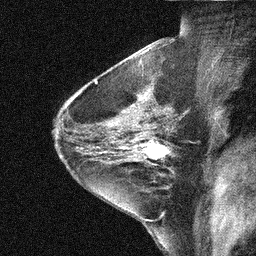
Breast MRI (dynamic contrast-enhanced), one sagittal slice; slice 29 of 44 in the series (ordered by position); dynamic contrast-enhanced study with each time point stored as its own series, time point 2 of 3 at this slice position (early post-contrast, ordered by acquisition time); 1.5 T; TE 5 ms, TR 10.3 ms; 3 mm slice thickness; 256 × 256 image matrix, field of view 180 × 180 mm. Patient: female, 31 years. Case-level facts recorded for this patient, not image findings: setting: breast cancer imaged before/during neoadjuvant chemotherapy; receptor status: HER2-positive.
Structures marked on this image (semi-automatic segmentation, software-assisted and operator-edited):
- analysis volume of interest (the breast-tissue region the enhancement analysis was run in; not a lesion): bounding box (x1, y1, x2, y2) in pixels: (136, 131, 181, 168)
- tumour enhancement mask (voxels above the 90 % enhancement threshold inside the analysis volume of interest): (140, 141, 172, 160)